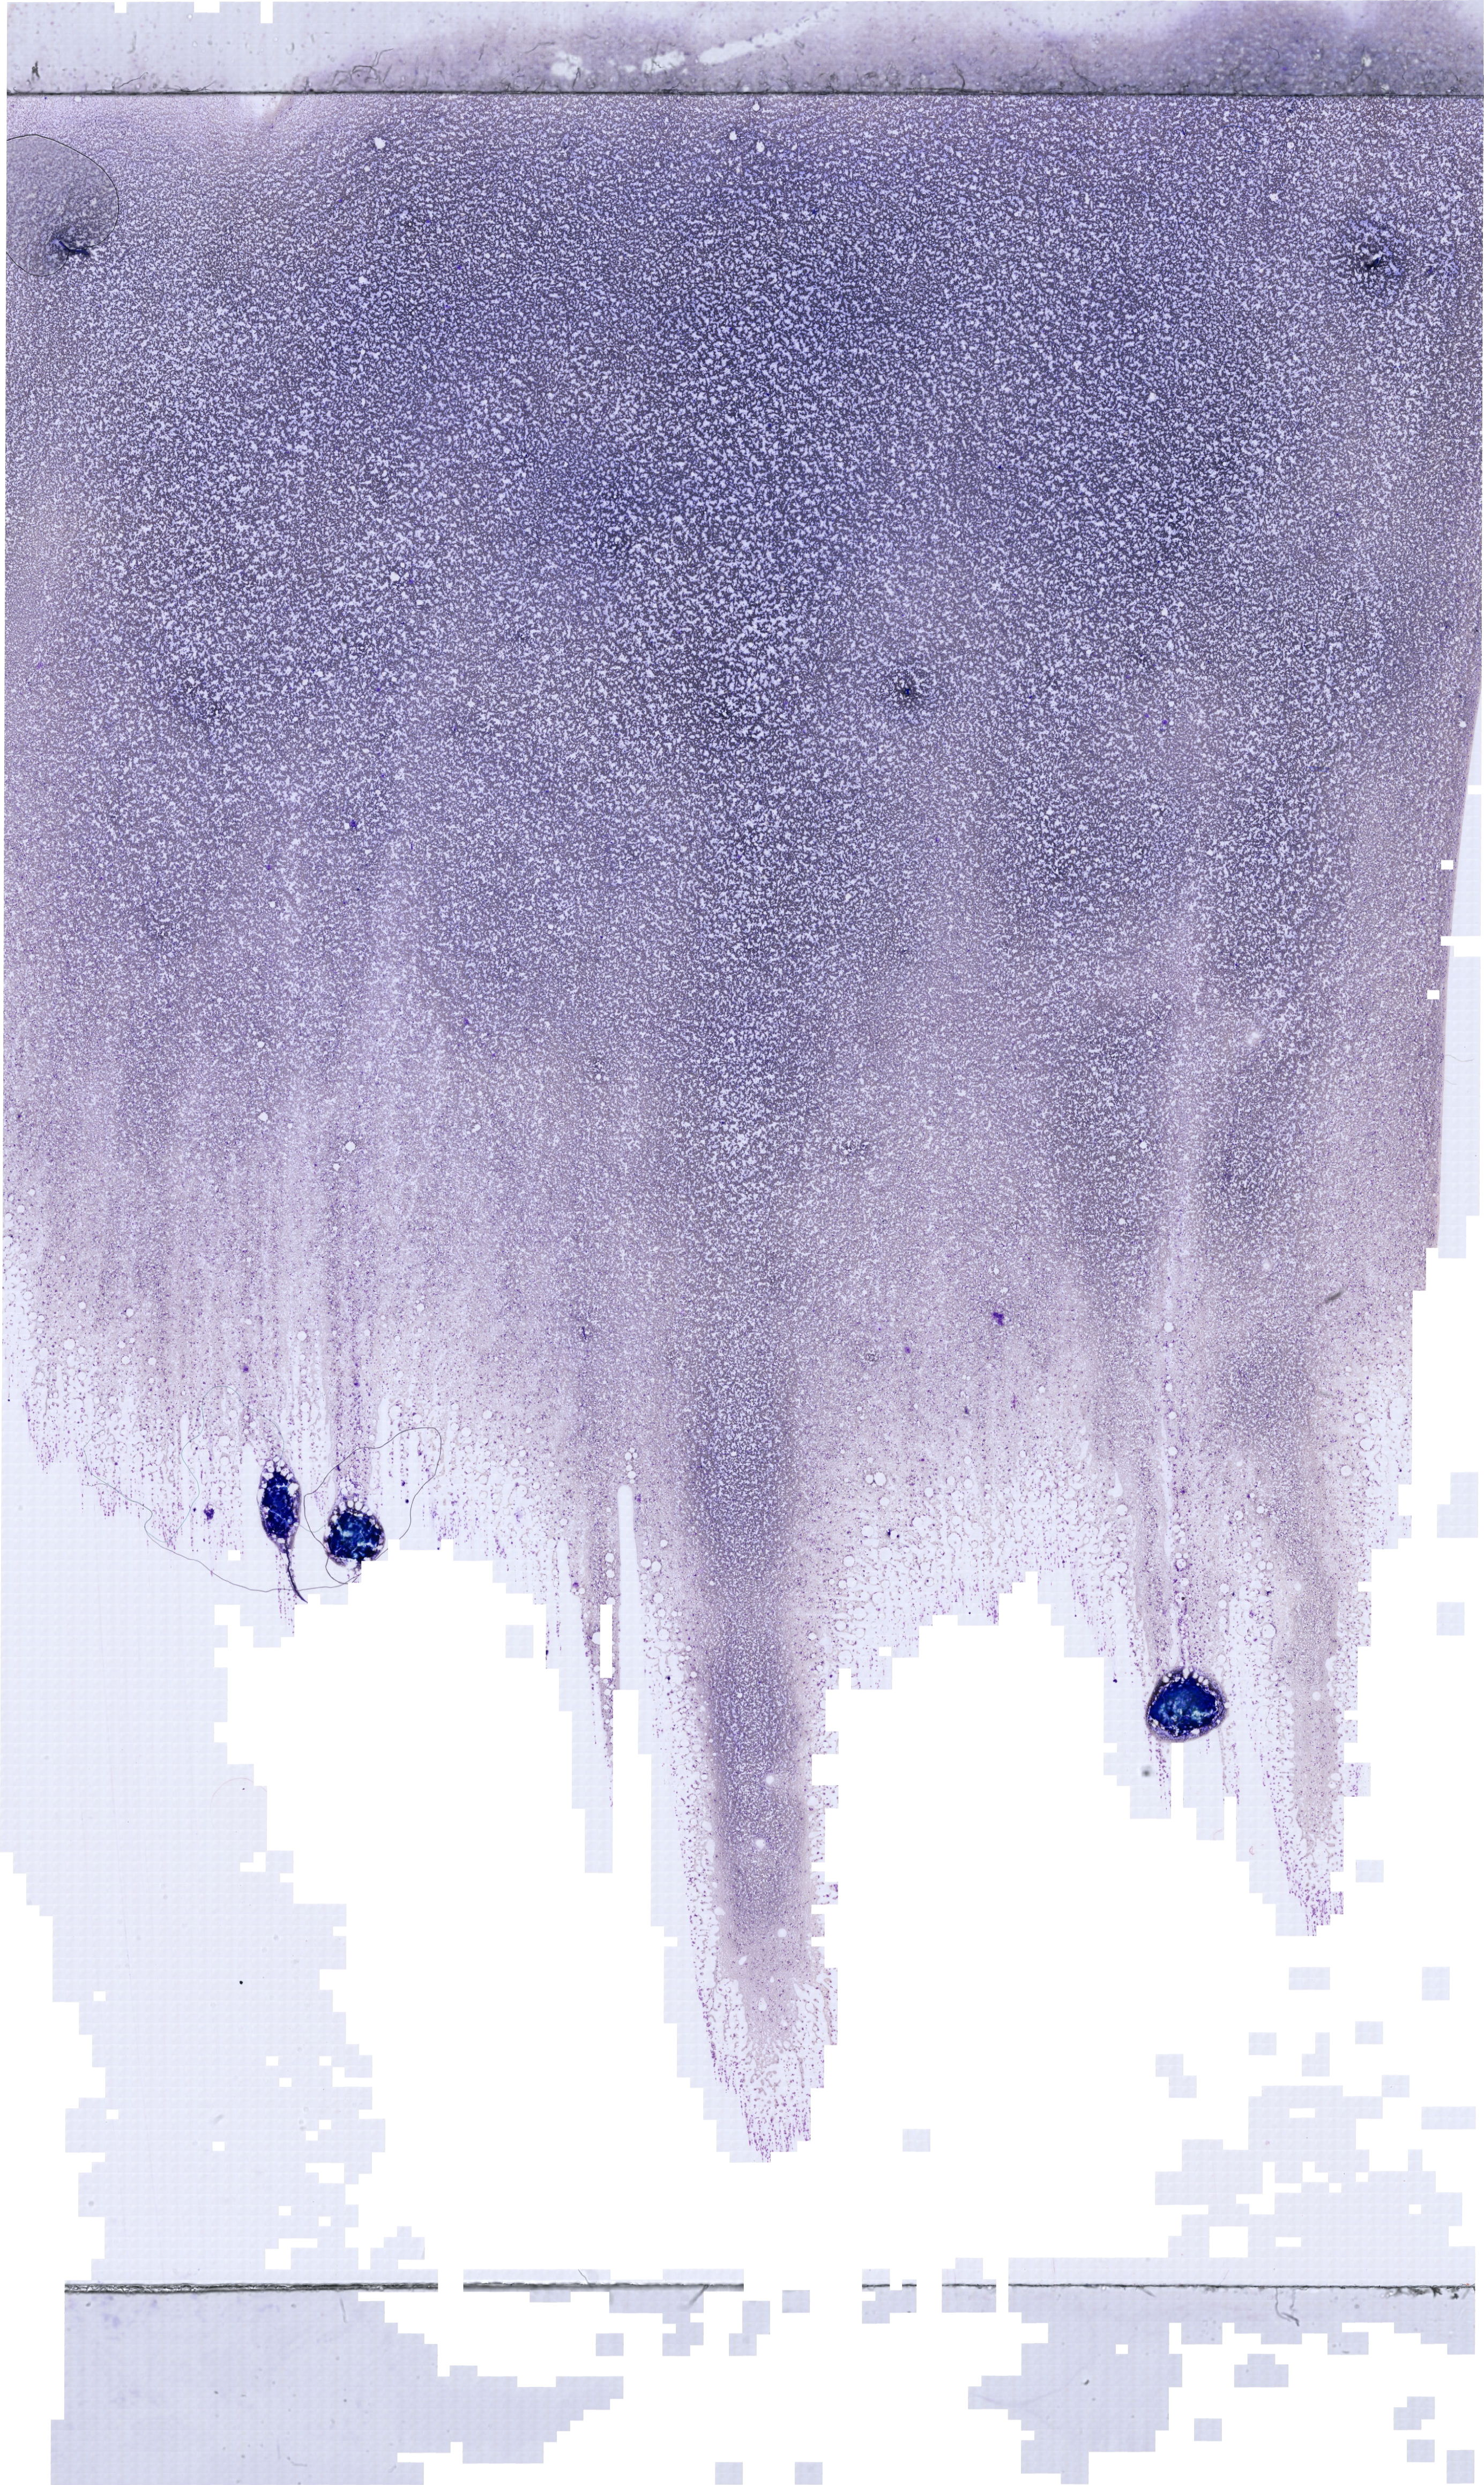
Bone marrow aspirate smear, May-Grünwald-Giemsa (MGG) stain, whole-slide image — low-resolution overview of the scanned area, about 21.6 x 36.2 mm. Patient sex: male.
* diagnosis: T Acute Lymphoblastic Leukemia